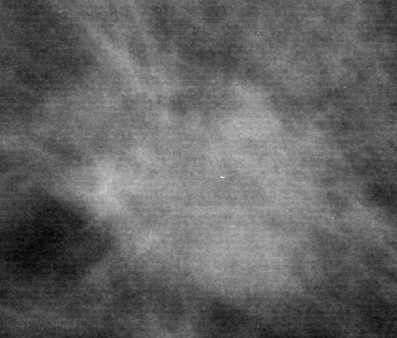
Crop from a digitized film mammogram around one marked abnormality; left breast; MLO view; BI-RADS breast density category 2 (scale 1–4).
Marked abnormality: mass, shape round, margins spiculated; BI-RADS assessment category 5; pathology (as recorded): malignant.